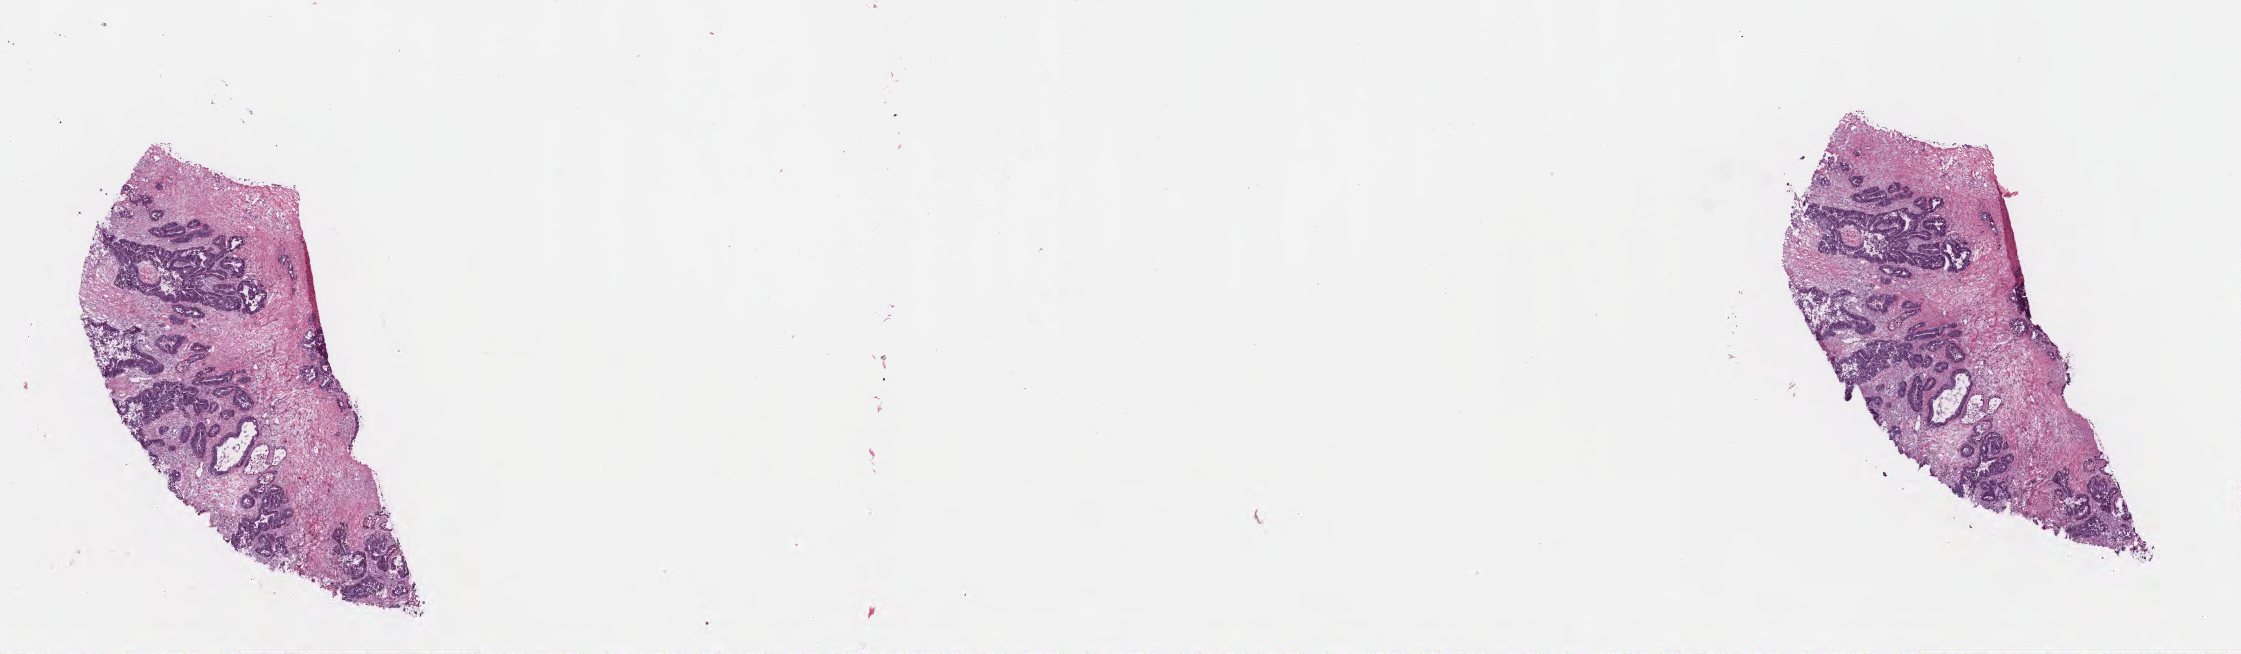
H&E whole-slide image — low-resolution overview of the scanned area, about 18.1 x 5.3 mm, cryosection, metastatic tumor tissue, resected from liver. Male, age 56 years at initial diagnosis. Slide review estimates, as recorded: tumor cells 85%, tumor nuclei 85%, stromal cells 14%, necrosis 1%, normal cells 0%. Infiltration values recorded for this section: lymphocyte infiltration 4%, monocyte infiltration 1%, neutrophil infiltration 5%.
* patient diagnosis (primary): Adenocarcinoma, metastatic, NOS